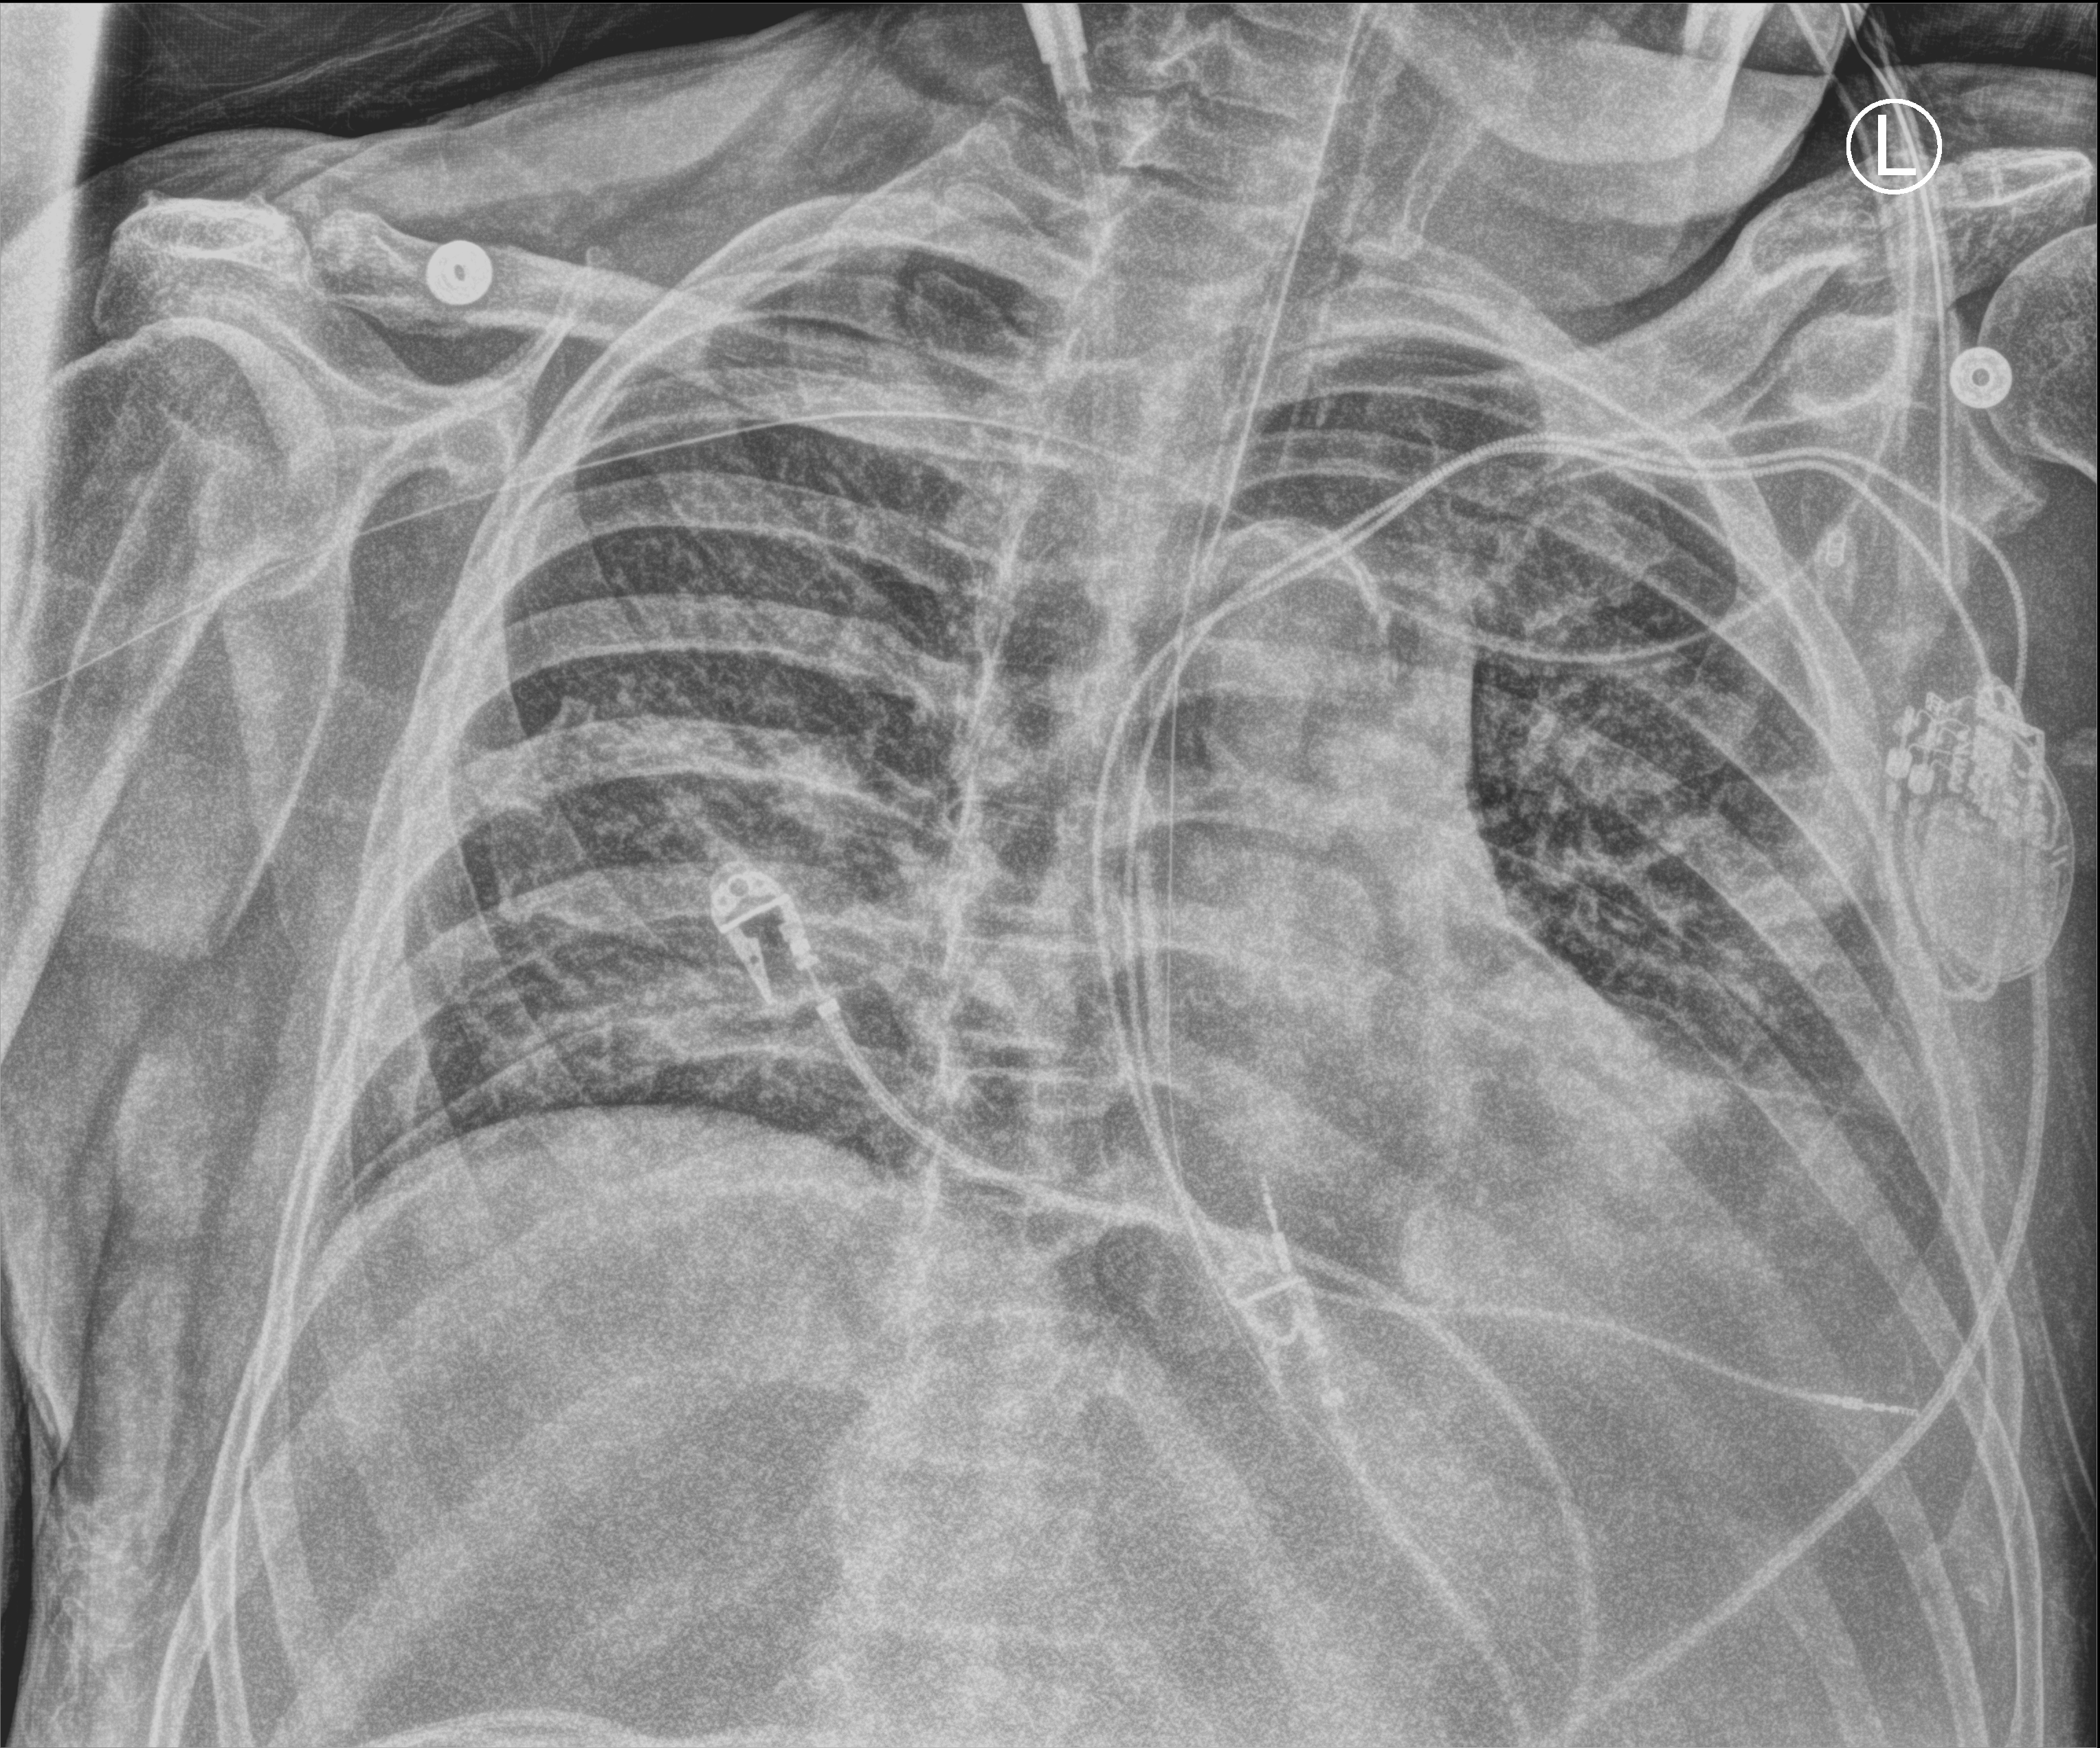
Portable chest radiograph, anteroposterior (AP) projection. Male patient hospitalised with COVID-19, age 60–74 years.
Admission-level facts for this patient (not findings on this image; timing relative to this image not recorded):
- admitted to intensive care during this hospital stay: yes